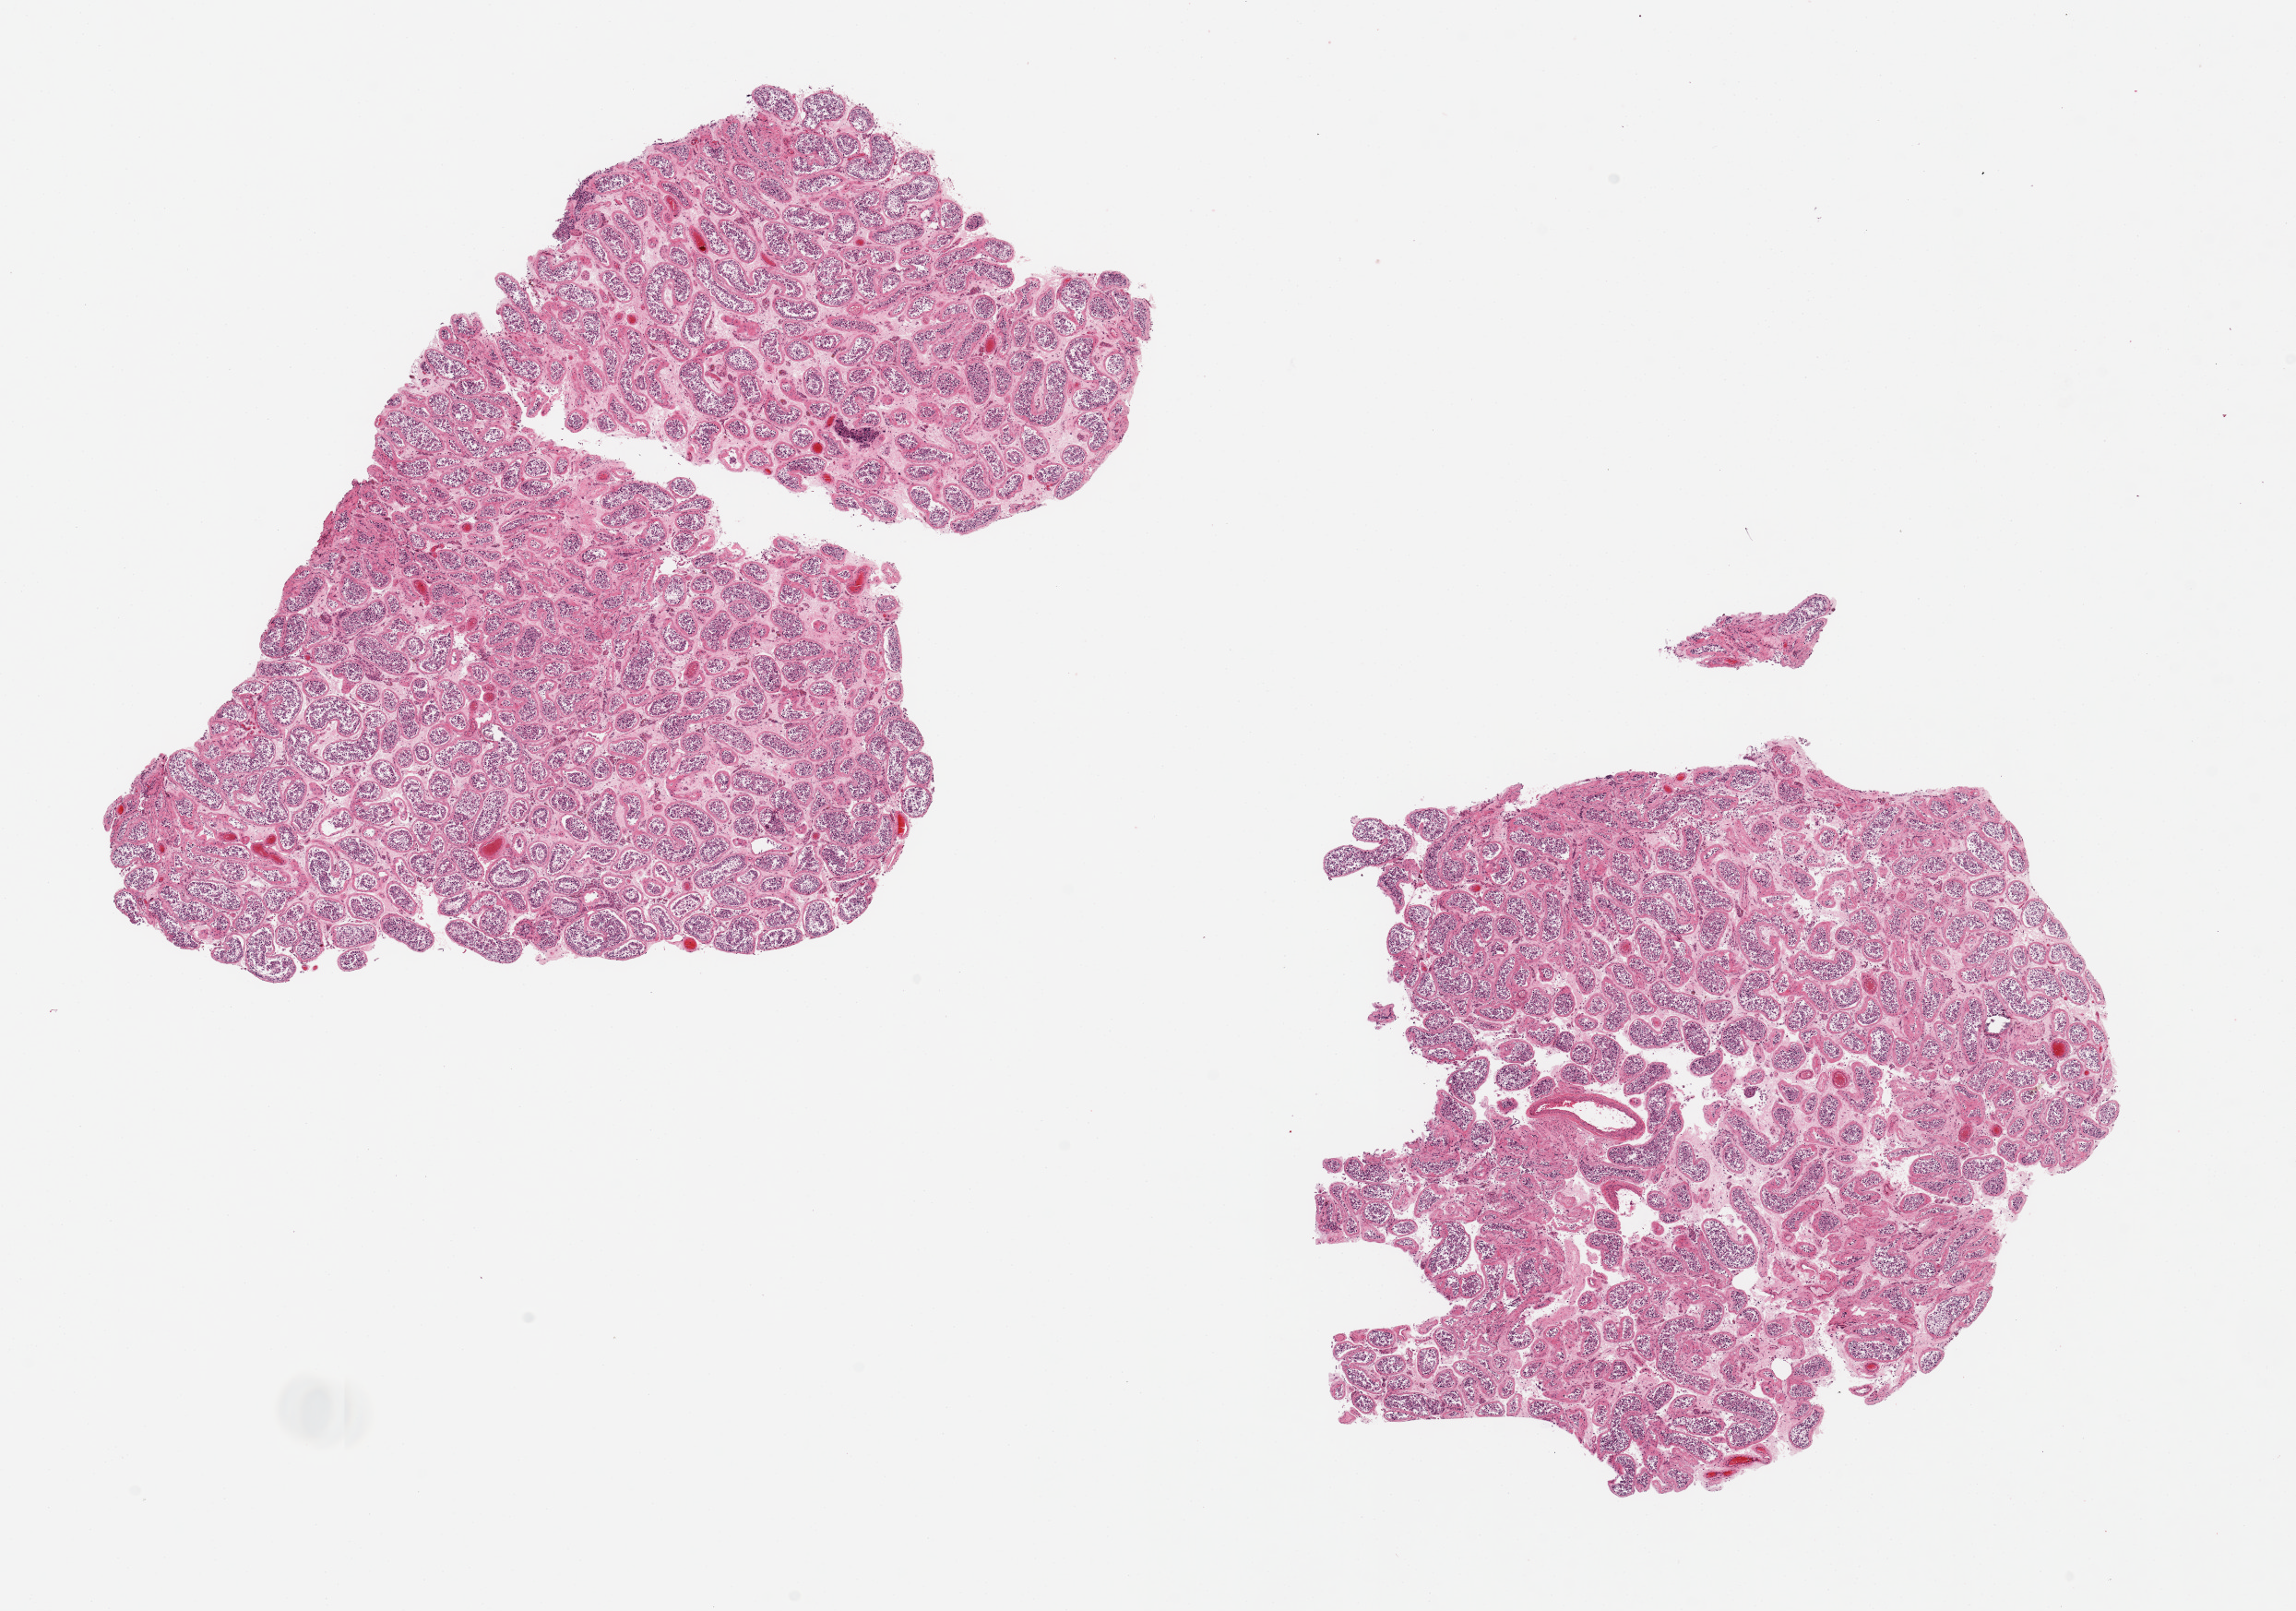
Whole-slide image, H&E stain, brightfield, a low-resolution overview of the entire scanned area, about 19.7 x 13.8 mm (slide scanned at 20x). PAXgene-fixed, paraffin-embedded tissue. Section of testis (target tissue). Donor tissue sample. Donor: male.
Pathologist's review note for this sample: 2 aliquots, ~7.5x6mm. probable spermatogenesis, autolysis compromises assessment.